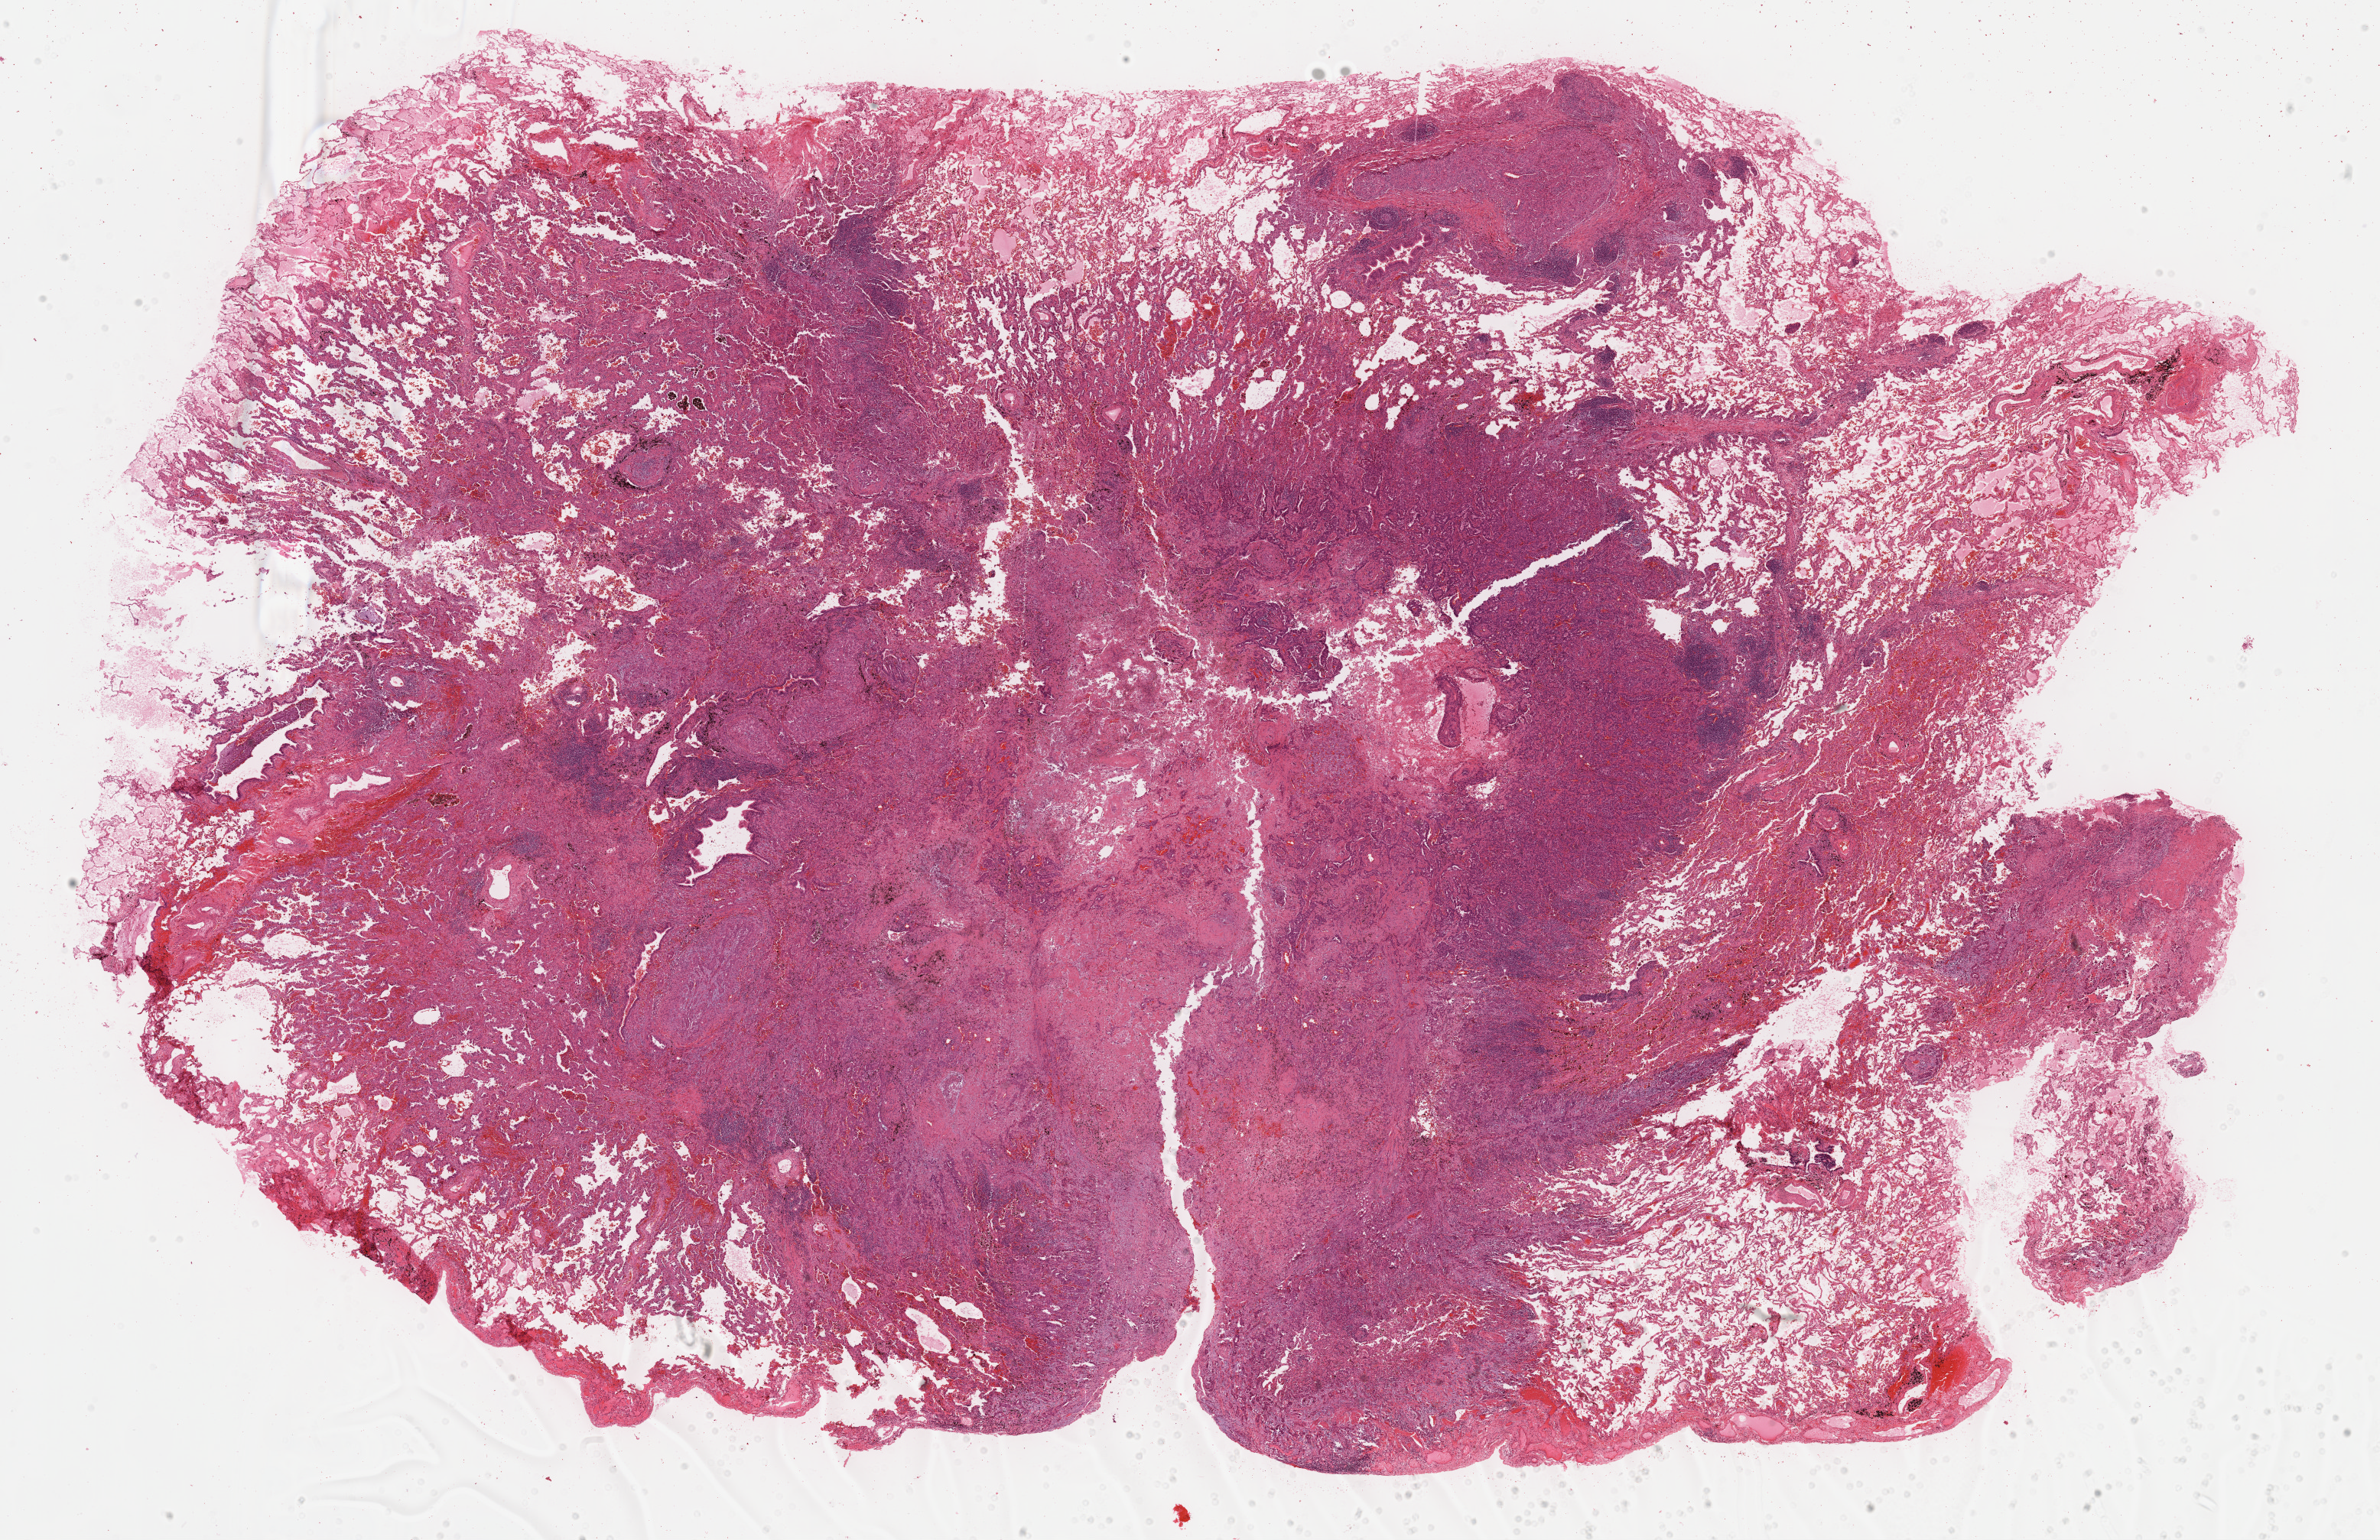
Whole-slide histology image, H&E, low-resolution overview of the scanned area, about 25.2 x 16.3 mm; formalin-fixed paraffin-embedded (FFPE) diagnostic section; lung, primary tumour sample. Male patient; age at initial diagnosis 49 years.
- AJCC pathologic stage: IA
- diagnosis: Acinar cell carcinoma